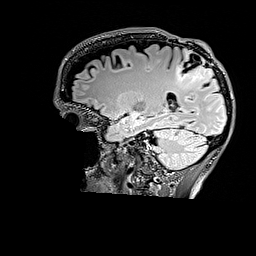
Brain MRI from a brain-tumour surgery series, one sagittal slice; position 113 of 176 along the scan axis; T2 FLAIR; 1 mm slice thickness; 256 × 256 image matrix. From the clinical record (not read from this slice): histopathology: Astrocytoma; WHO grade: 3; IDH mutation: yes; tumour location: Right Parietal.
Structures marked on this image (outlined manually by an expert reader):
- tumour: bounding box [x1, y1, x2, y2] px = [175, 50, 215, 85]
- tumour: [187, 59, 214, 82]